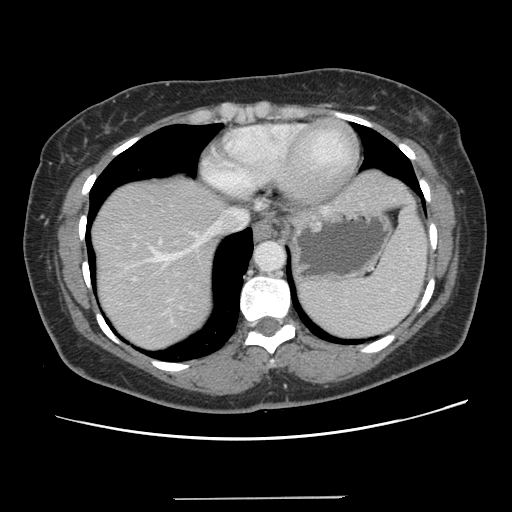
Contrast-enhanced abdominal CT, one axial slice. 120 kVp. Intravenous contrast given. Soft-tissue window (W 400 / L 40 HU). 2.5 mm slice thickness. 512 × 512 image matrix. Female patient, age 53 years. From the clinical record (not read from this slice): diagnosis: colorectal cancer liver metastases, imaged before liver resection; multiple liver metastases: no; largest metastasis: 14.5 cm.
Annotated regions visible in this slice (expert manual segmentation):
- hepatic veins: bounding box <113,208,247,278> (left, top, right, bottom; pixels)
- liver: <92,170,410,350>
- planned liver remnant (the part of the liver to remain after resection): <92,212,221,350>
- portal vein (with intrahepatic branches): <159,240,163,244>